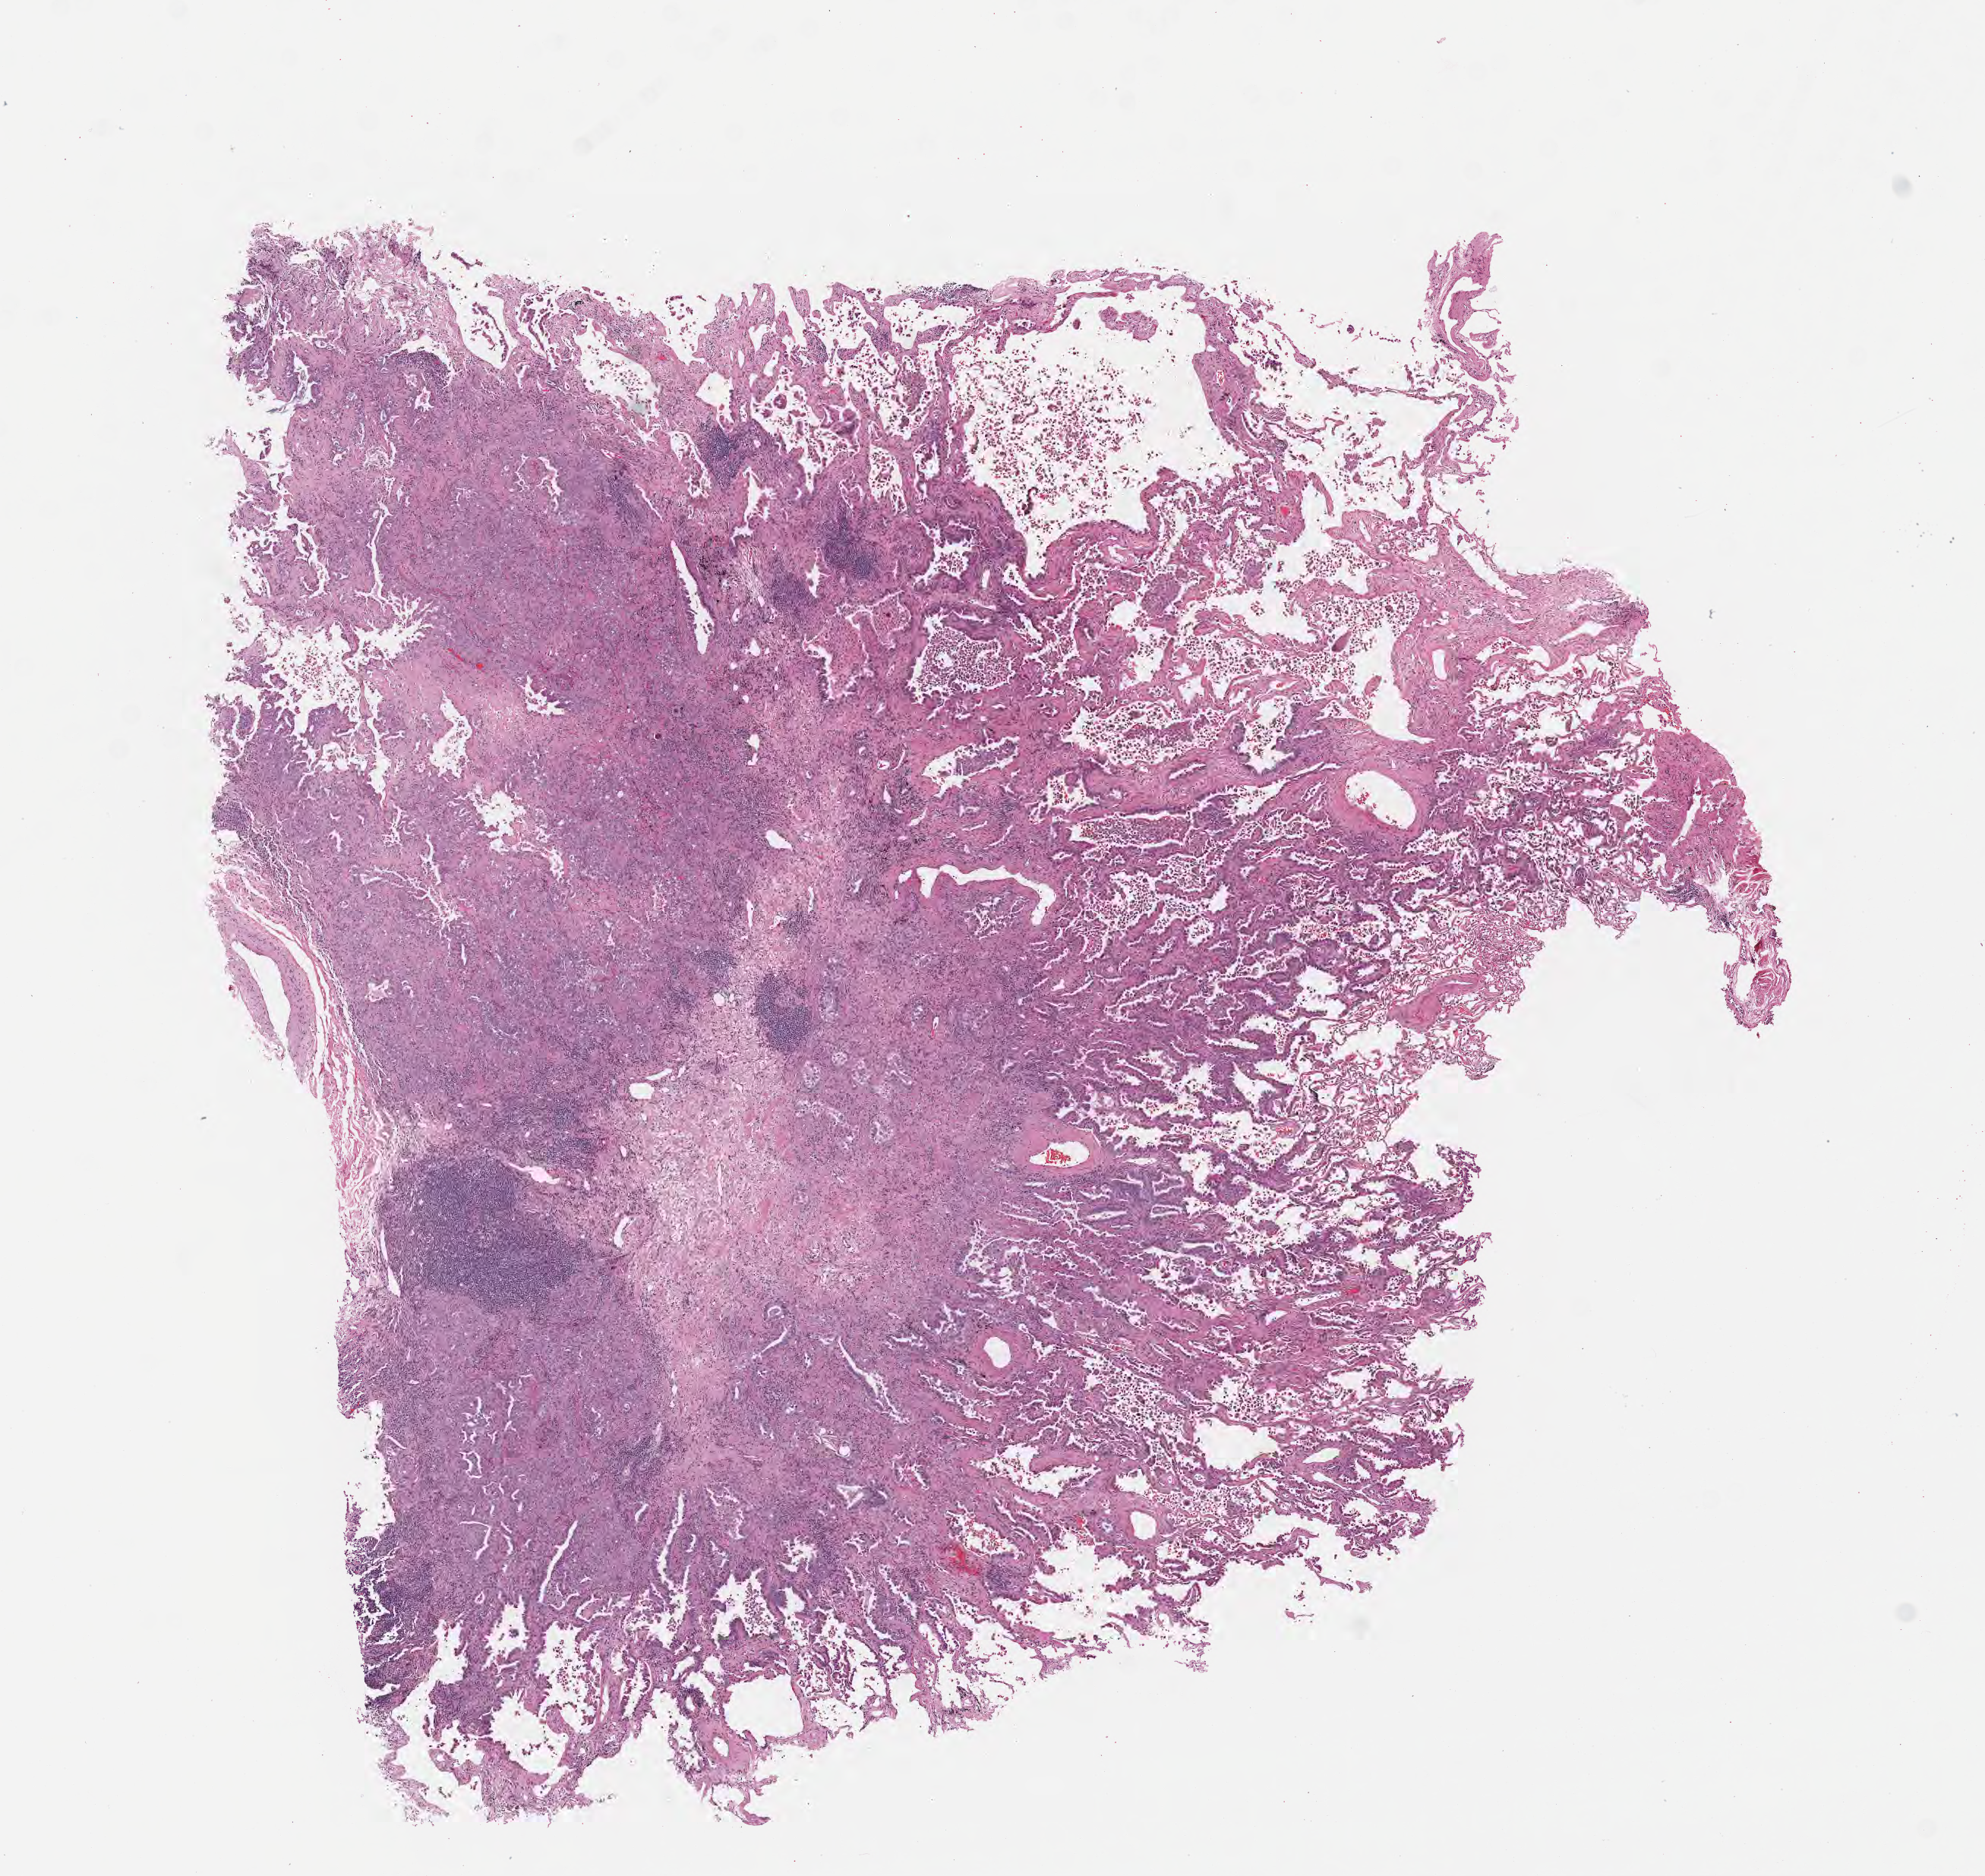
Hematoxylin and eosin (H&E) whole-slide image — low-resolution overview of the scanned area, about 10.6 x 10.0 mm. Formalin-fixed paraffin-embedded section. Specimen: primary tumor. Site: upper lobe of right lung. Patient: male, age at initial diagnosis 82 years.
Histologic diagnosis: Adenocarcinoma, NOS.